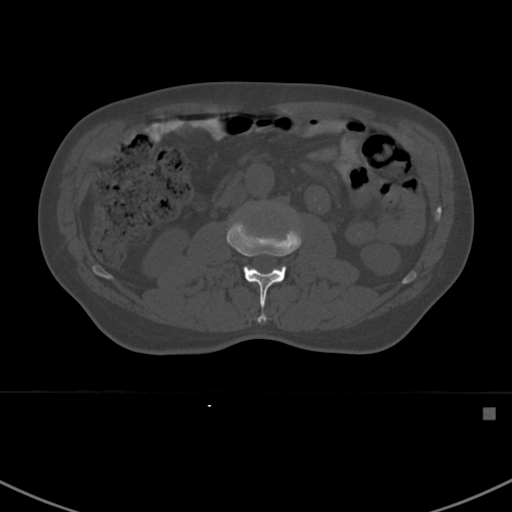
CT including the spine, one axial slice; position 282 of 412 along the scan axis; bone window (W 1800 / L 400 HU); 1.5 mm slice thickness; 512 × 512 image matrix. Patient: male, 59 years. From the clinical record (not read from this slice): primary cancer: prostate.
Structures marked on this image (semi-automatically segmented with operator editing):
- L2 vertebra: bounding box [x1, y1, x2, y2] px = [227, 213, 302, 322]